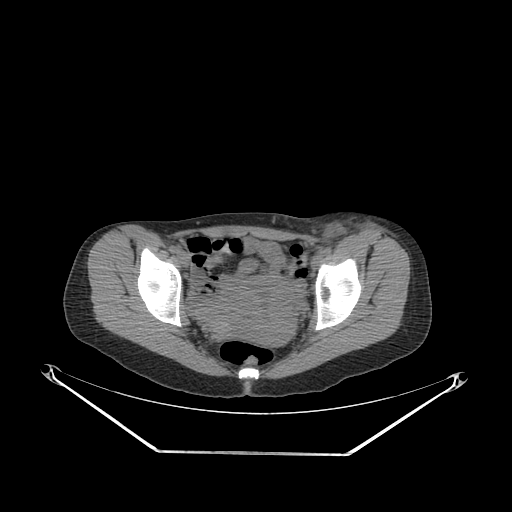
CT of an extremity soft-tissue mass (from a PET/CT study), one axial slice. Position 77 of 267 along the scan axis. Reconstruction kernel SOFT. Soft-tissue window (W 400 / L 40 HU). 3.75 mm slice thickness. 512 × 512 image matrix. Female patient. Case-level facts recorded for this patient, not image findings: histological type: leiomyosarcoma; grade: high; site of the primary tumour: groin.
Outlined on this slice (expert contour drawn on MRI and transferred to this co-registered scan by the dataset authors):
- gross tumour volume including surrounding oedema: bounding box (x1, y1, x2, y2) in pixels: (292, 221, 396, 254)
- gross tumour volume (mass): (320, 235, 346, 254)